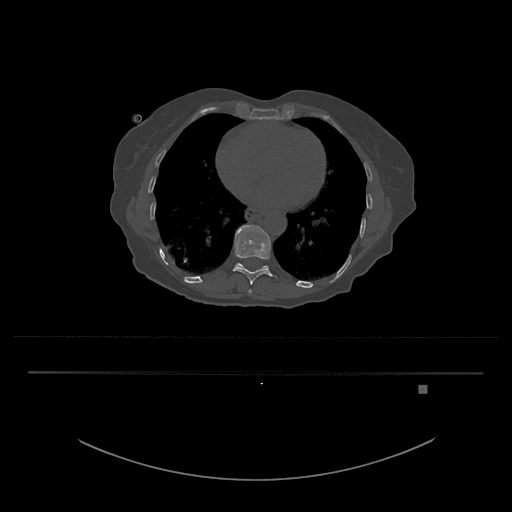
CT including the spine, one axial slice; position 706 of 797 along the scan axis; bone window (W 1800 / L 400 HU); 0.5 mm slice thickness; 512 × 512 image matrix. Female patient, age 57 years. Case-level facts recorded for this patient, not image findings: primary cancer: cervical.
Structures marked on this image (semi-automatically segmented with operator editing):
- T10 vertebra: bounding box (x1, y1, x2, y2) in pixels: (233, 224, 272, 285)
- T11 vertebra: (236, 263, 268, 269)
- T9 vertebra: (249, 289, 252, 293)